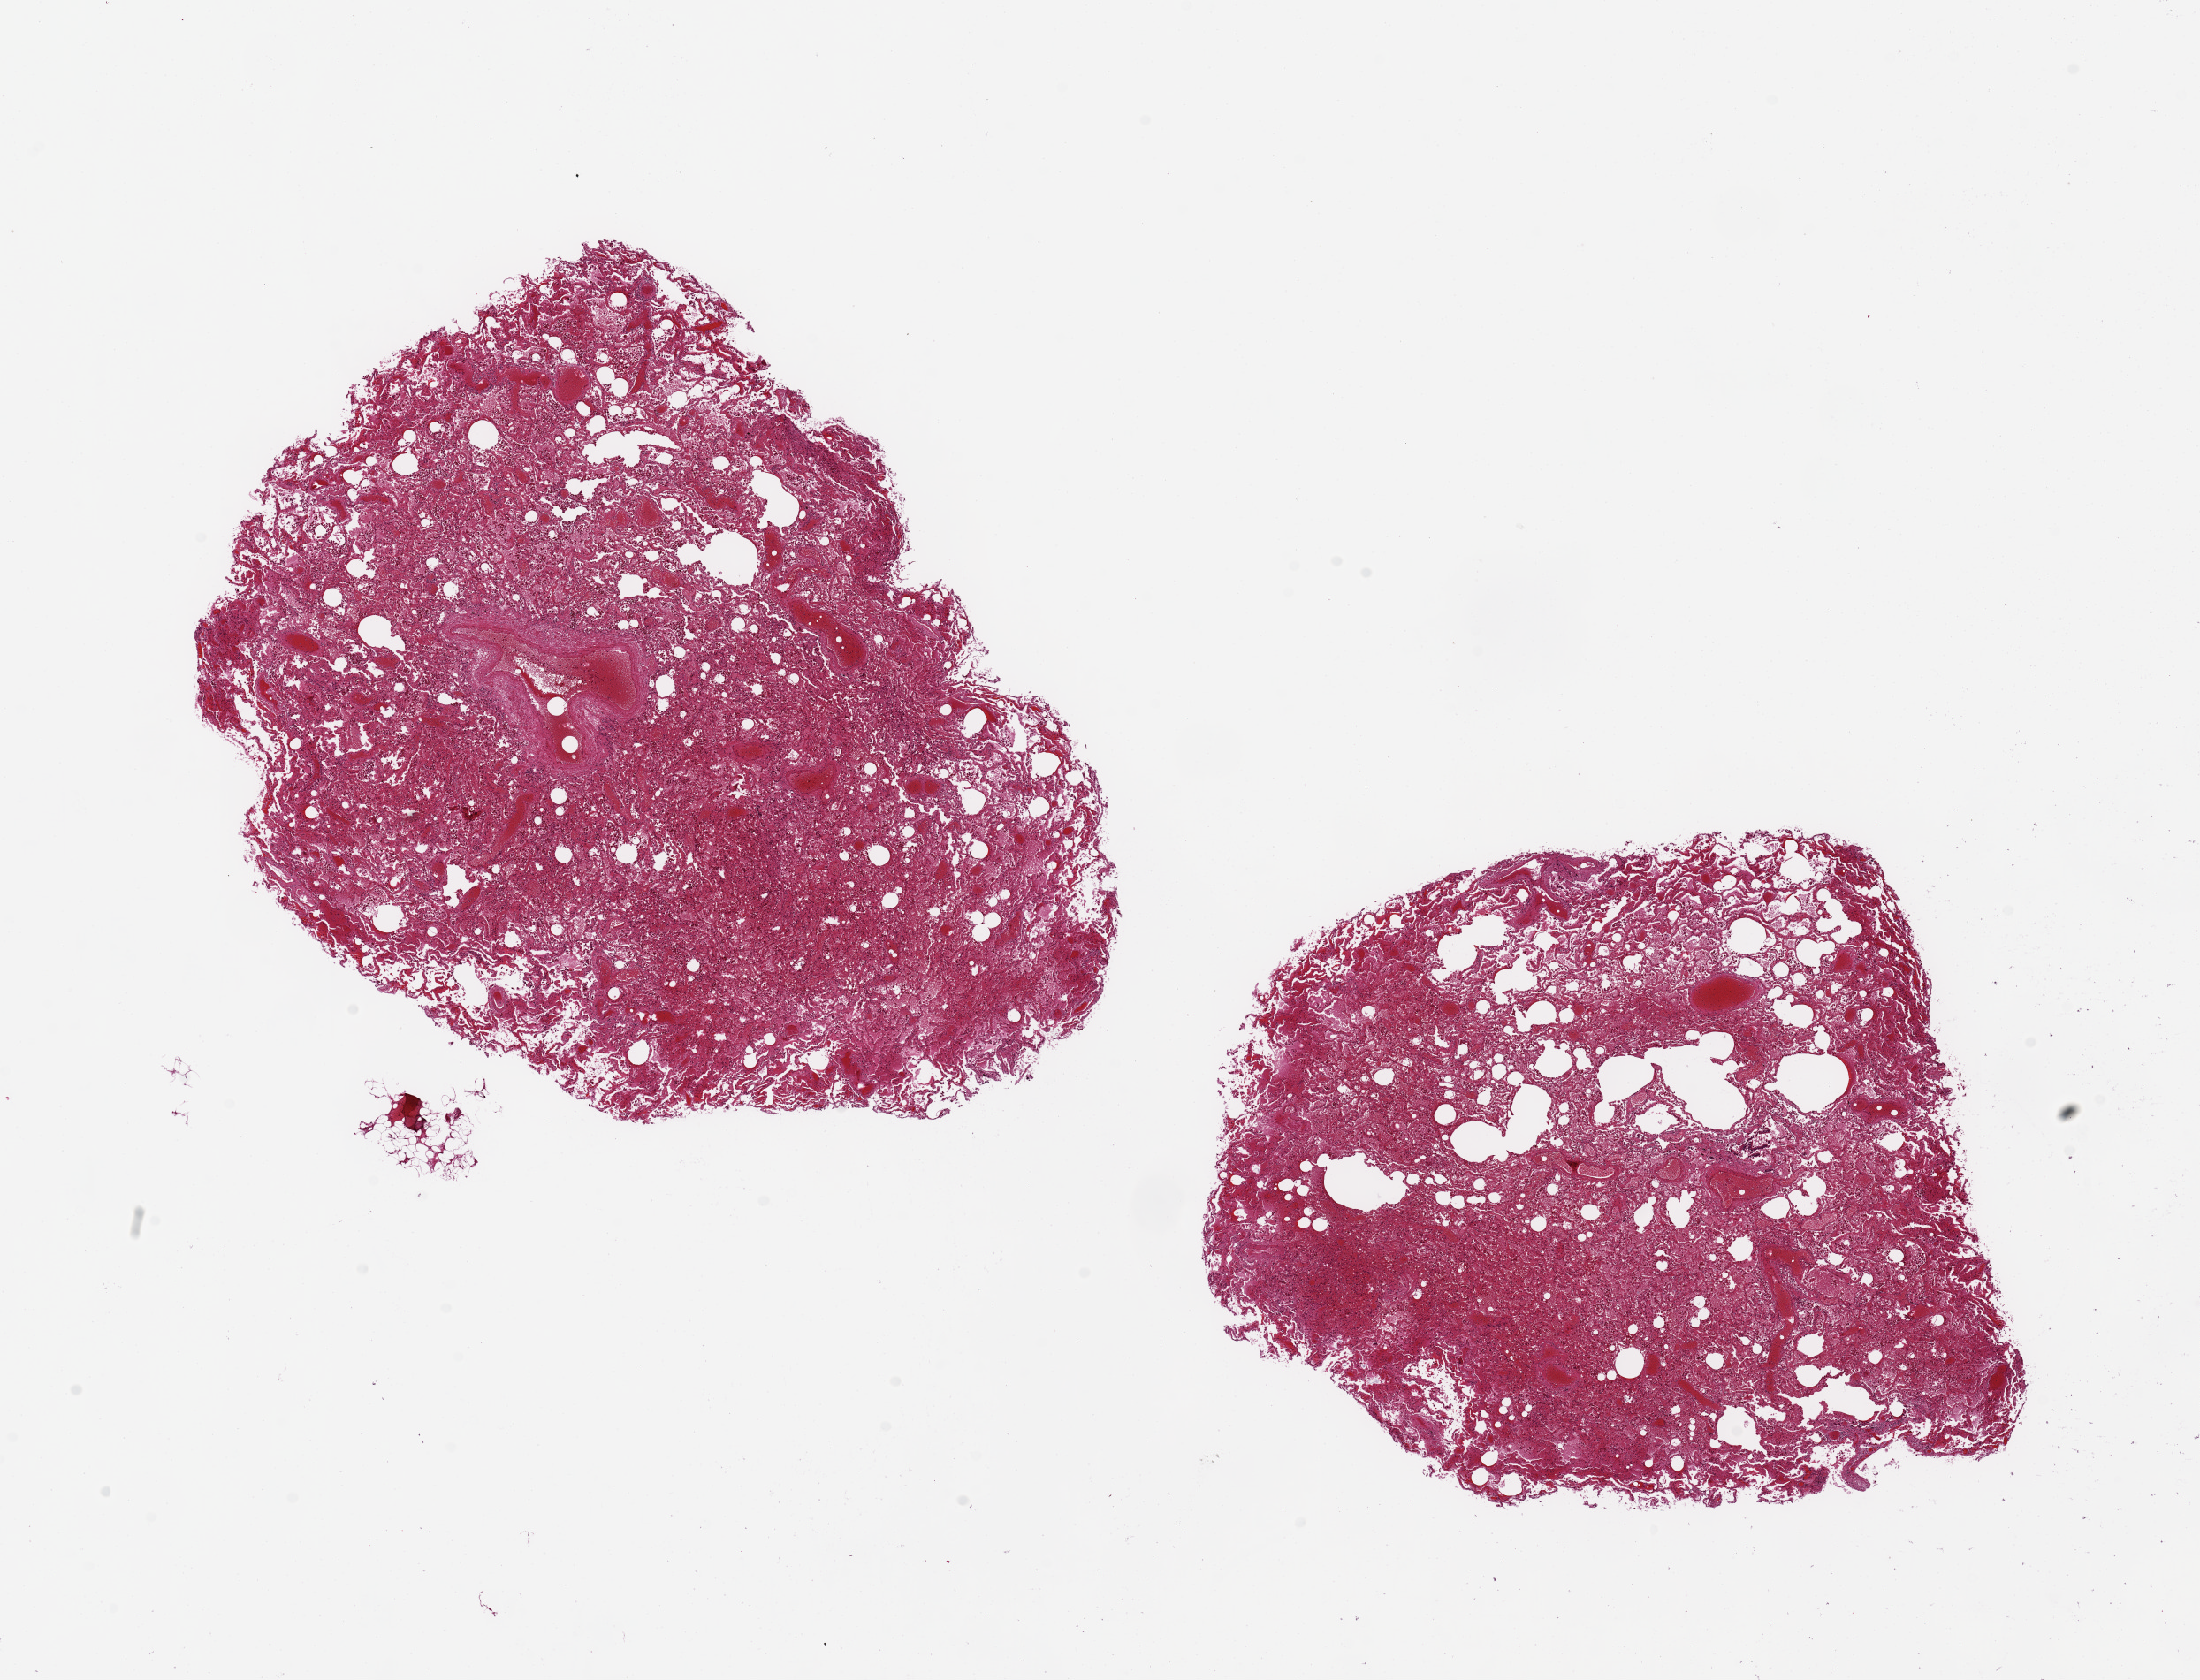
Haematoxylin and eosin whole-slide image — whole scanned area (about 19.7 x 15.0 mm) shown as a low-resolution overview, PAXgene-fixed, paraffin-embedded tissue, section of lung (target tissue), tissue donor sample.
• review note (as recorded): 2 pieces ~7x6mm. Diffuse severe congestion/edema, badly autolyzed